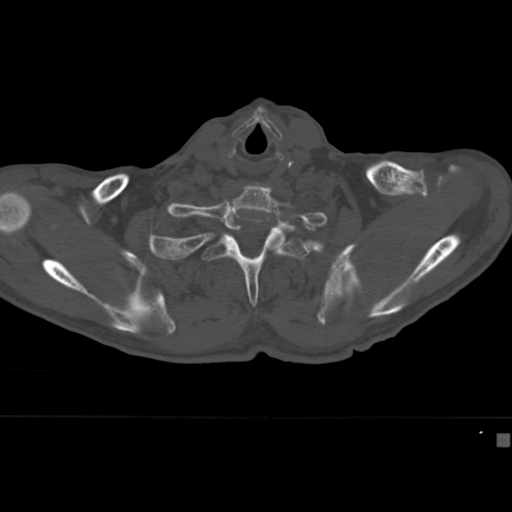
CT including the spine, one axial slice; slice 348 of 430 in the series (ordered by position); bone window (W 1800 / L 400 HU); 512 × 512 image matrix, field of view 337 × 337 mm. Male patient, age 64 years. From the clinical record (not read from this slice): primary cancer: uterus; vertebrae with lytic lesions (as recorded): T1, T4, T5, T7, L5.
Annotated regions visible in this slice (semi-automatic segmentation, software-assisted and operator-edited):
- T2 vertebra: bounding box (x1, y1, x2, y2) in pixels: (201, 235, 310, 307)